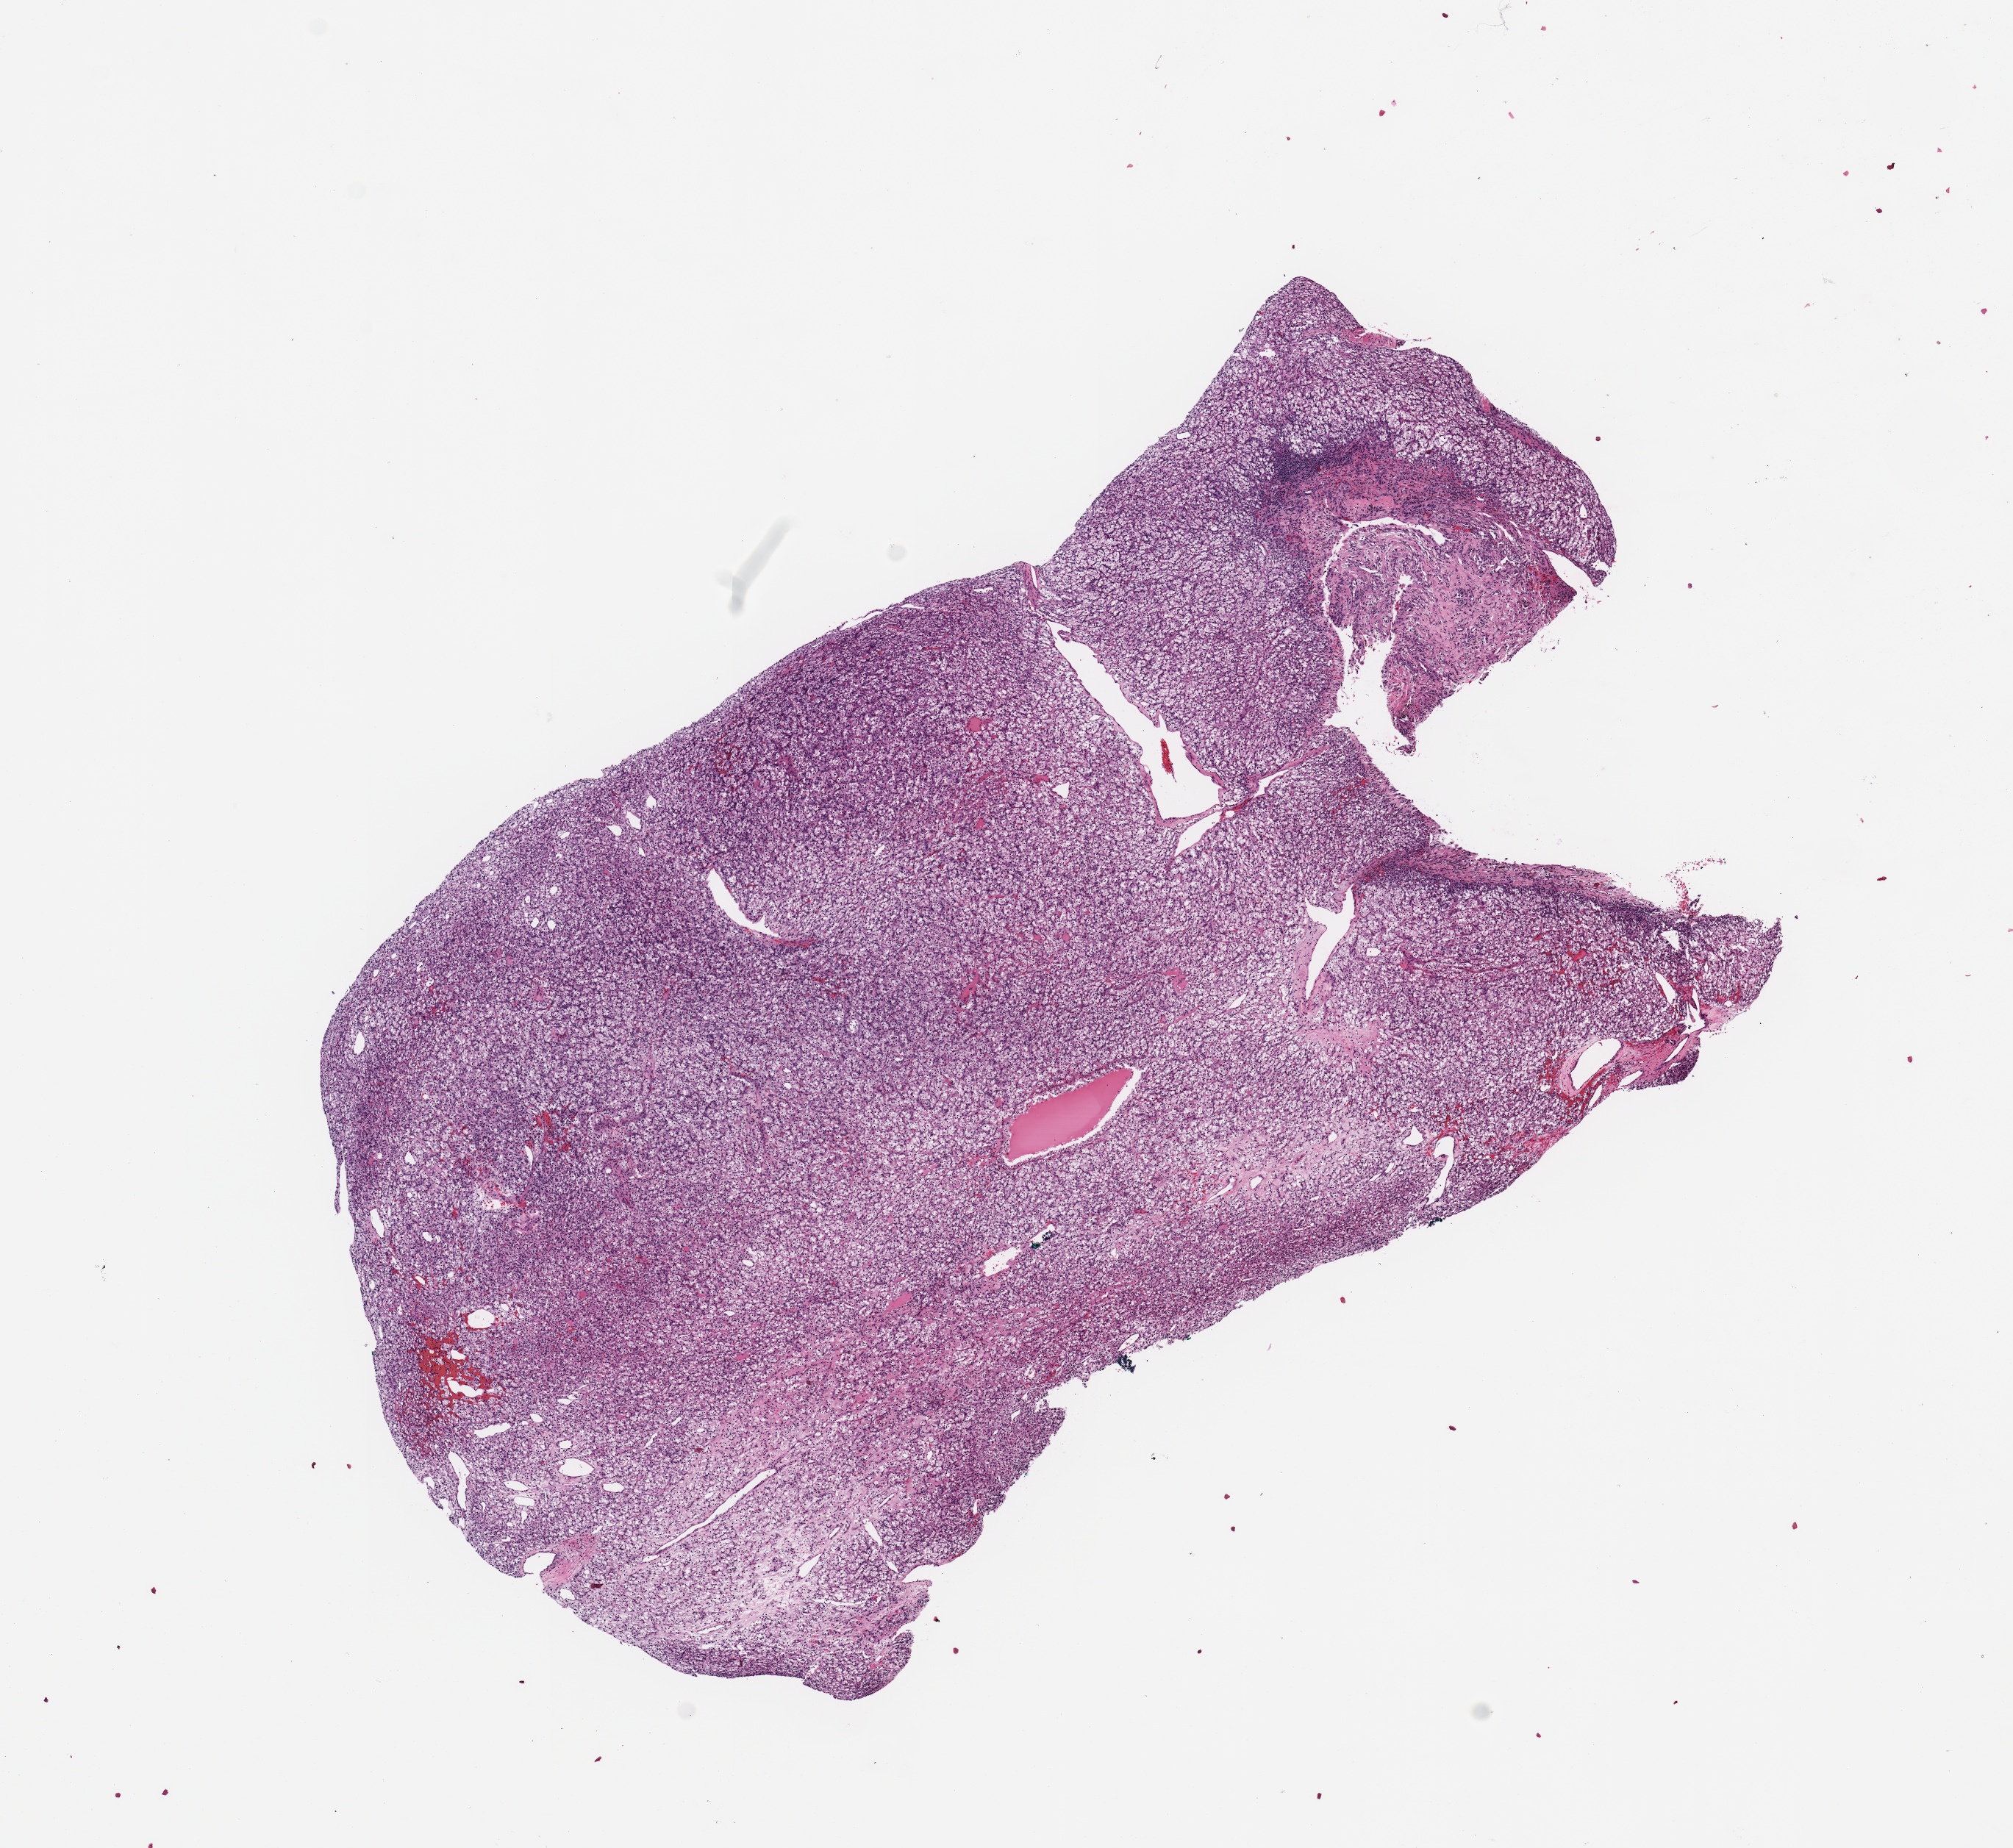
H&E whole-slide image, shown as a low-resolution overview of the whole scanned area (about 10.8 x 9.9 mm, slide scanned at 20x). Tumour tissue sample, kidney. Patient: female, age 59 years. Histologic grade: G2 (moderately differentiated).
- primary tumour site (as recorded): lower pole
- diagnosis: Renal cell carcinoma, NOS
- AJCC pathologic stage: I